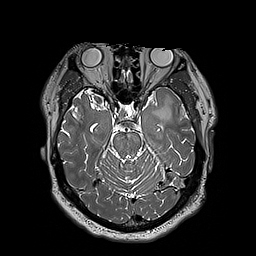
Brain MRI from a brain-tumour surgery series, one axial slice; position 126 of 192 along the scan axis; 256 × 256 image matrix, field of view 250 × 250 mm. From the clinical record (not read from this slice): histopathology: Astrocytoma; WHO grade: 3; IDH mutation: yes; tumour location: Left Insular.
Annotated regions visible in this slice (expert manual segmentation):
- tumour: box from (x=153, y=99) to (x=172, y=122) px